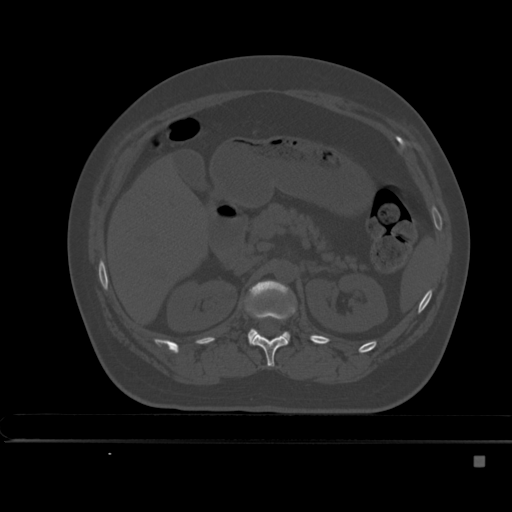
CT including the spine, one axial slice; slice 206 of 495 in the series (ordered by position); bone window (W 1800 / L 400 HU); 1.5 mm slice thickness; 512 × 512 image matrix, field of view 404 × 404 mm. Patient: female, 33 years. Case-level facts recorded for this patient, not image findings: primary cancer: breast.
Structures marked on this image (semi-automatically segmented with operator editing):
- L1 vertebra: bounding box <246,280,292,345> (left, top, right, bottom; pixels)
- T12 vertebra: <252,301,296,367>